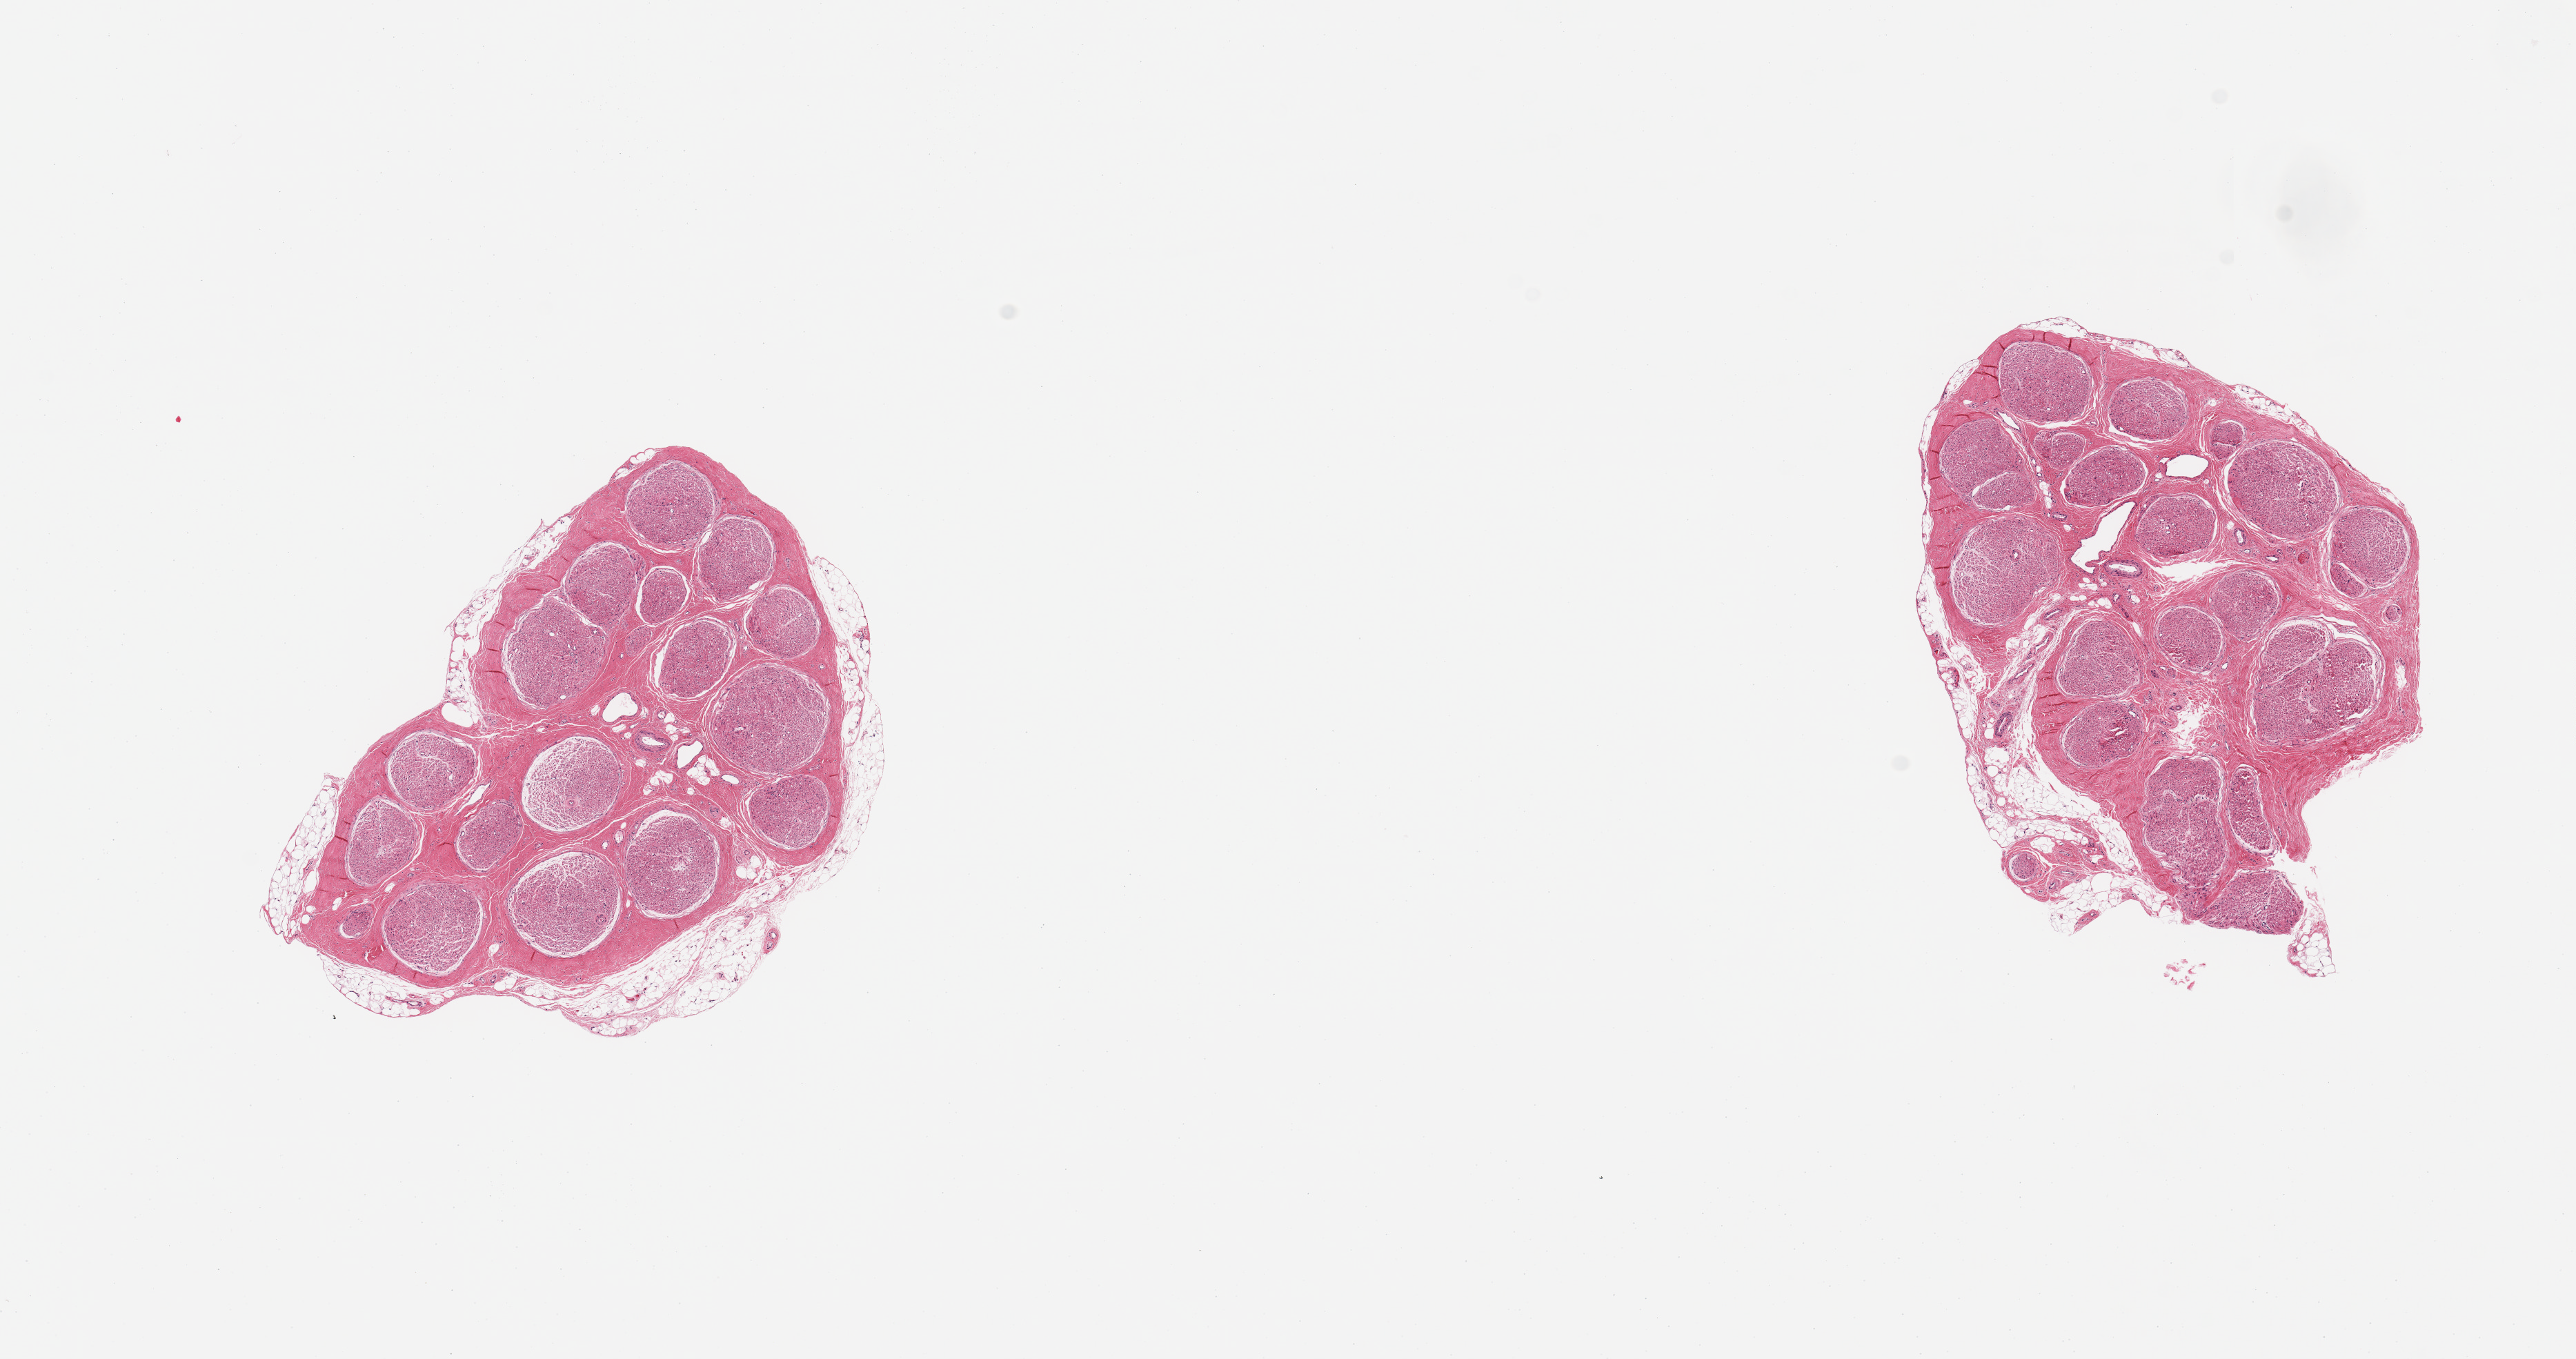
Haematoxylin and eosin whole-slide image, brightfield — a low-resolution overview of the entire scanned area, about 14.8 x 7.8 mm, PAXgene-fixed paraffin-embedded (PFPE) section, target tissue: tibial nerve, tissue donor sample. Male donor.
Pathologist's review note for this sample: 2 pieces; well trimmed: 10% external fat.